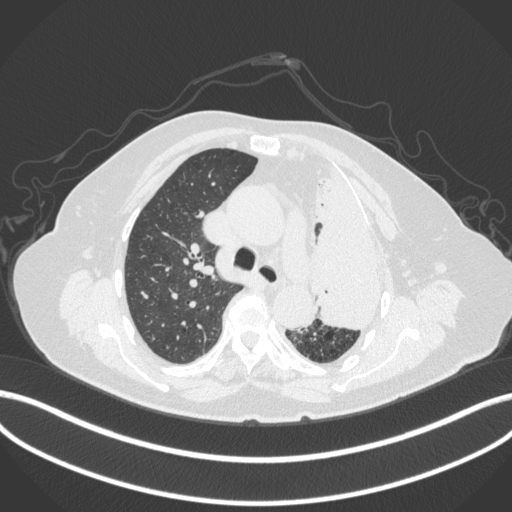
Chest CT, one axial slice. Position 273 of 399 along the scan axis. Lung window (W 1500 / L -600 HU). 512 × 512 image matrix, field of view 400 × 400 mm. Female patient, age 75 years. Case-level facts recorded for this patient, not image findings: clinical TNM (as recorded): T3 N3 M1.
Annotated regions visible in this slice (rectangle marked by the reading radiologist):
- lung tumour (recorded histology: adenocarcinoma): bounding box <311,162,398,332> (left, top, right, bottom; pixels)